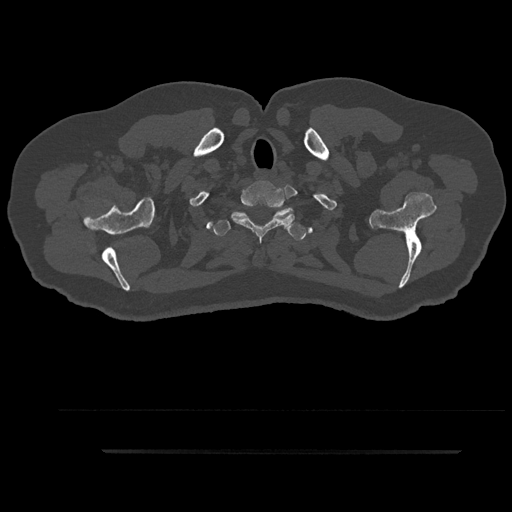
CT including the spine, one axial slice; slice 786 of 797 in the series (ordered by position); reconstruction kernel Br40s/3; 120 kVp; bone window (W 1800 / L 400 HU); 512 × 512 image matrix. Male patient, age 63 years. Case-level facts recorded for this patient, not image findings: primary cancer: renal; vertebrae with lytic lesions (as recorded): T8.
Outlined on this slice (semi-automatic segmentation, software-assisted and operator-edited):
- T1 vertebra: bounding box [x1, y1, x2, y2] px = [231, 185, 294, 242]
- T2 vertebra: [212, 207, 306, 241]